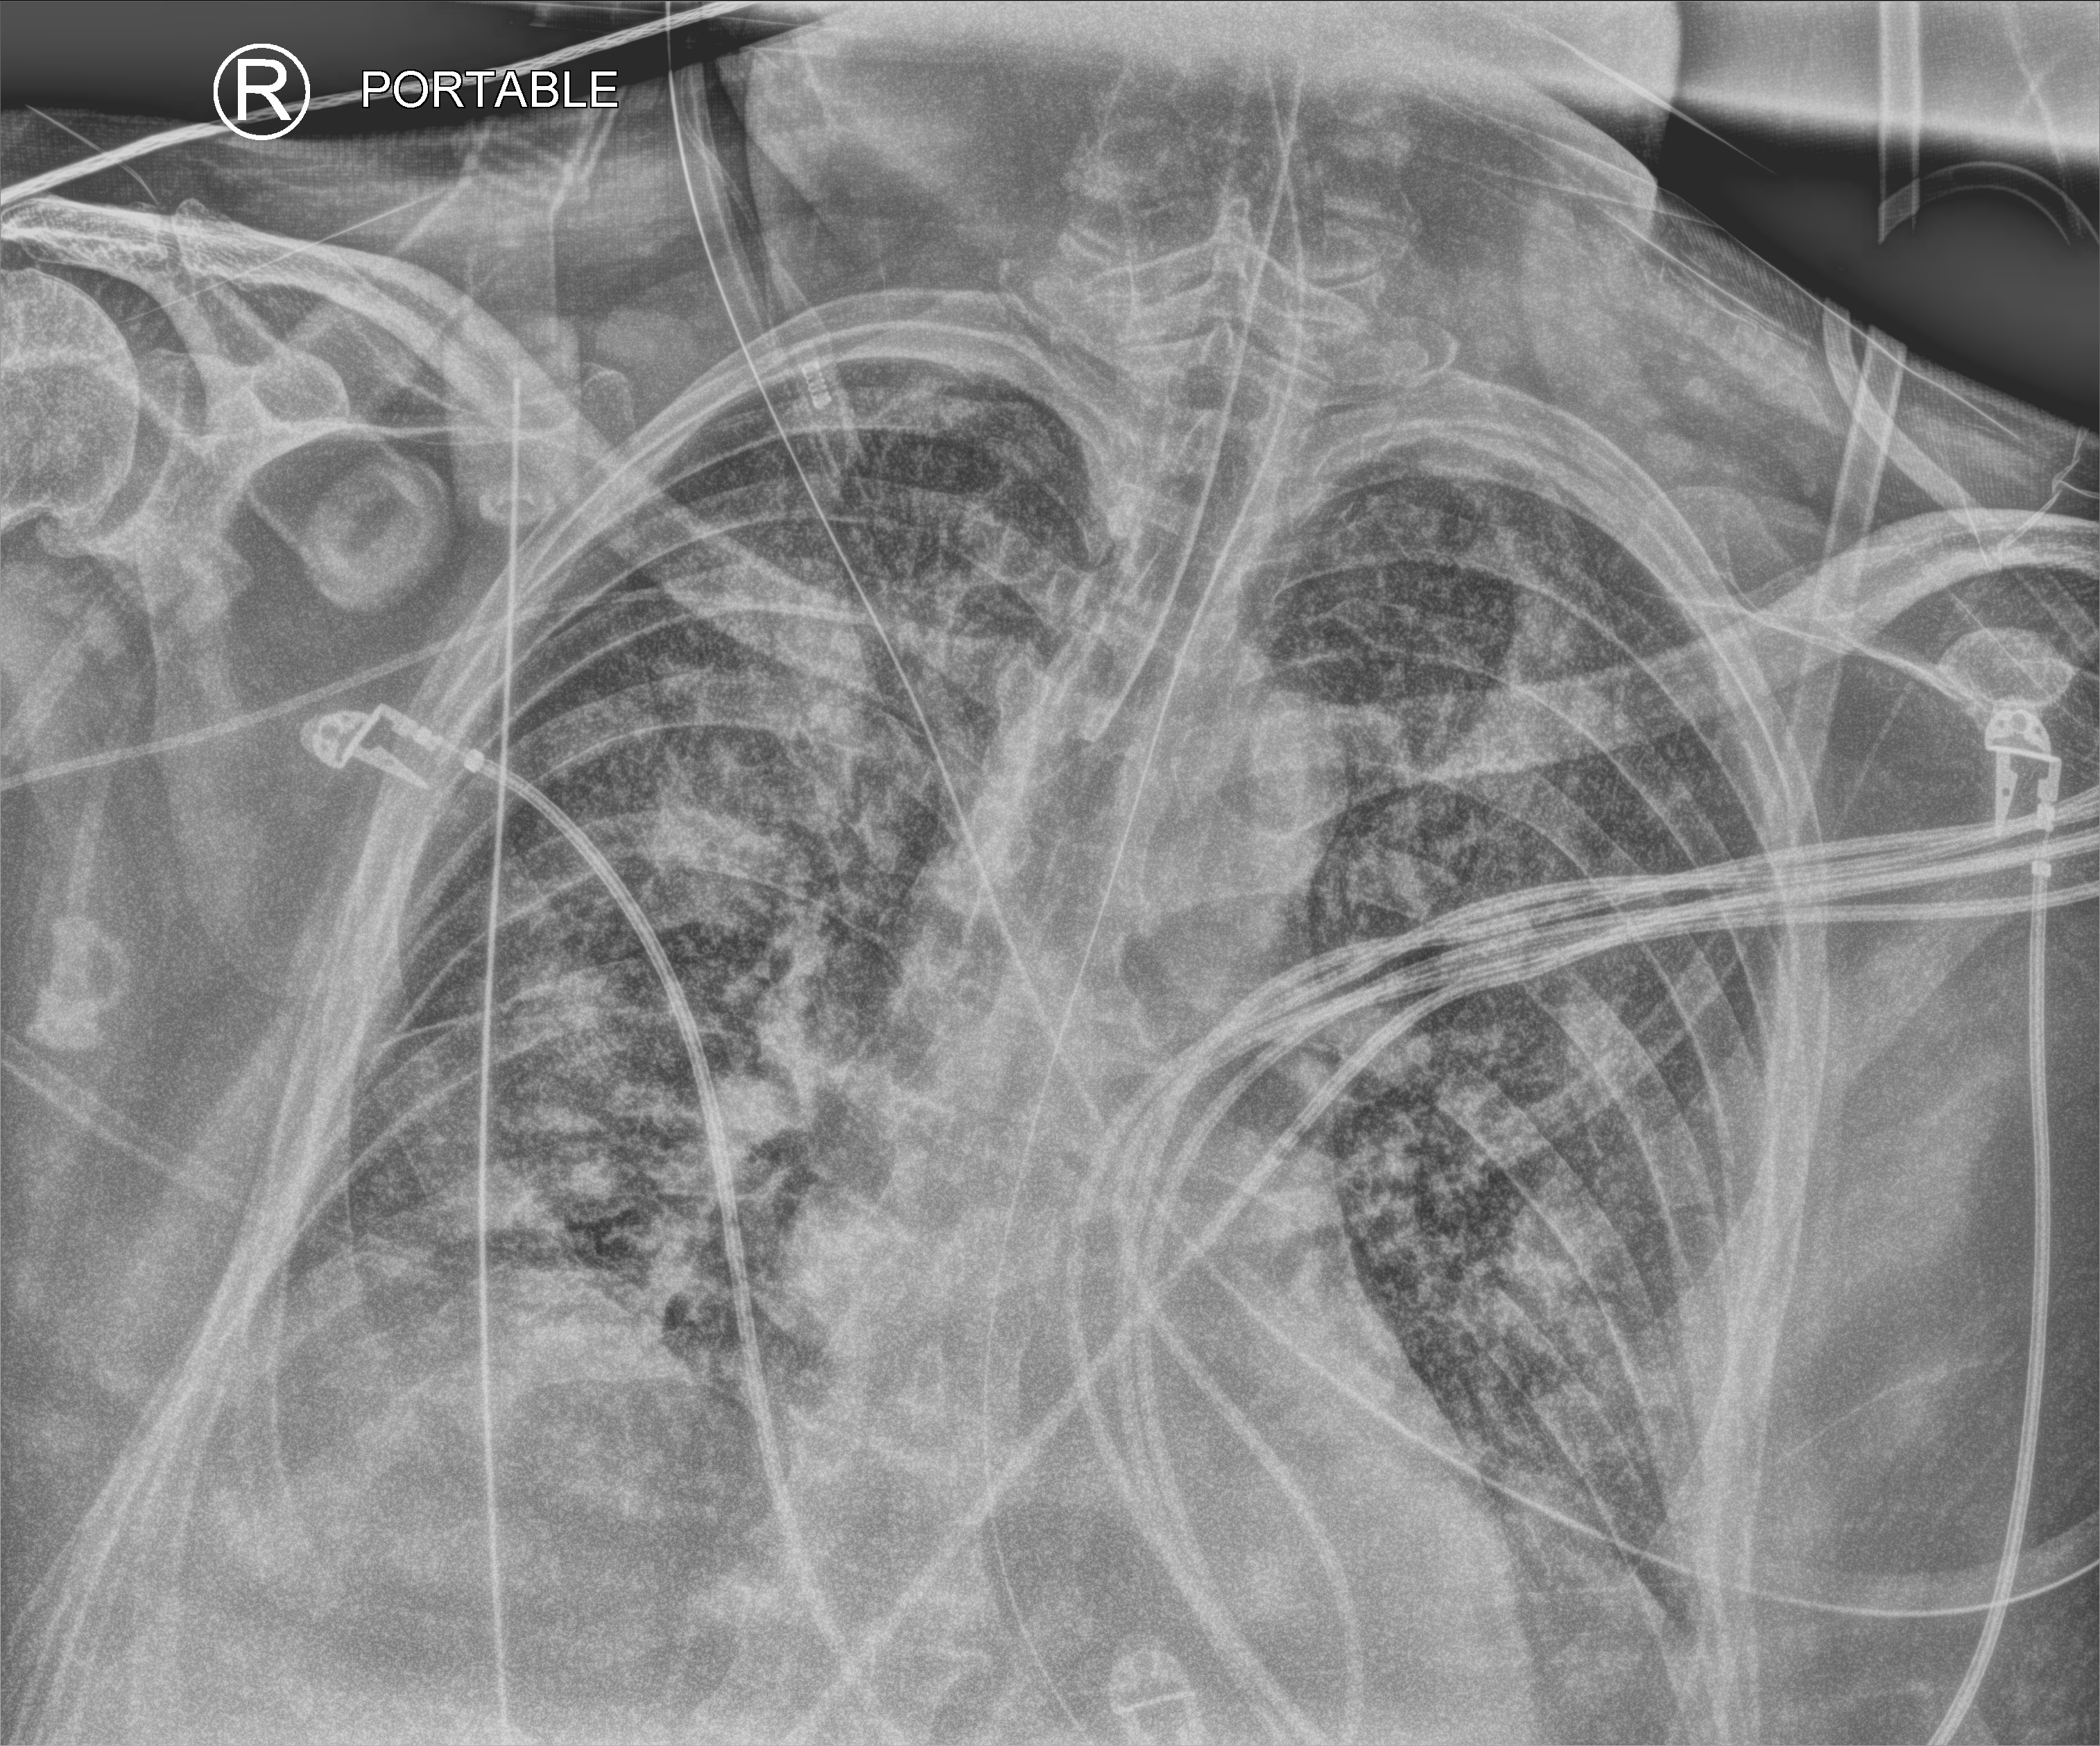
Bedside chest radiograph (computed radiography); anteroposterior (AP) projection. Patient hospitalised with COVID-19; male, aged 60–74 years.
From the hospital-stay record, not from the radiograph (when in the stay this image was taken is not recorded): COPD (admission record): no.